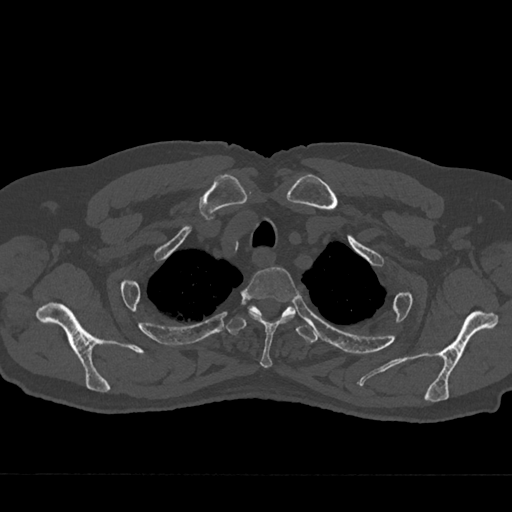
CT including the spine, one axial slice; position 594 of 797 along the scan axis; reconstruction kernel Br40s/3; bone window (W 1800 / L 400 HU); 0.5 mm slice thickness; 512 × 512 image matrix. Patient: male, 75 years. Case-level facts recorded for this patient, not image findings: primary cancer: renal; vertebrae with lytic lesions (as recorded): T4.
Structures marked on this image (semi-automatically segmented with operator editing):
- T2 vertebra: bounding box (x1, y1, x2, y2) in pixels: (242, 267, 299, 368)
- T3 vertebra: (226, 306, 318, 343)